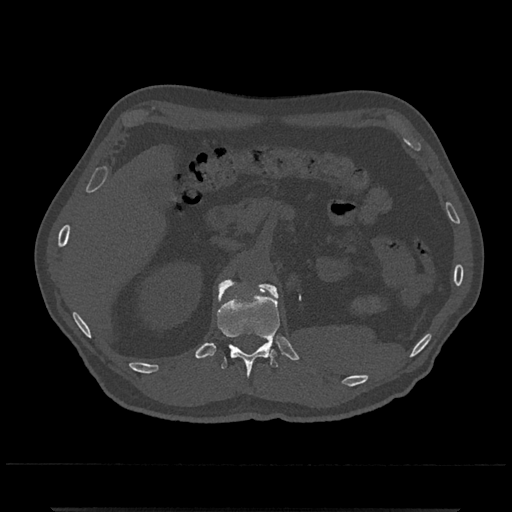
CT including the spine, one axial slice; position 419 of 797 along the scan axis; reconstruction kernel Br40s/3; bone window (W 1800 / L 400 HU); 0.5 mm slice thickness; 512 × 512 image matrix. Patient: male, 67 years. Case-level facts recorded for this patient, not image findings: primary cancer: prostate.
Annotated regions visible in this slice (semi-automatically segmented with operator editing):
- L1 vertebra: bounding box <223,281,277,296> (left, top, right, bottom; pixels)
- T12 vertebra: <217,280,280,378>